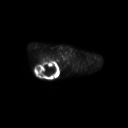
FDG PET of an extremity soft-tissue mass (from a PET/CT study), one axial slice. Slice 209 of 267 in the series (ordered by position). 3.27 mm slice thickness. 128 × 128 image matrix, field of view 700 × 700 mm. Patient: male, 61 years. Case-level facts recorded for this patient, not image findings: histological type: pleiomorphic spindle cell undifferentiated; grade: high; site of the primary tumour: right parascapusular.
Structures marked on this image (expert contour drawn on MRI and transferred to this co-registered scan by the dataset authors):
- gross tumour volume including surrounding oedema: box from (x=34, y=60) to (x=60, y=77) px
- gross tumour volume (mass): (x=35, y=60)–(x=58, y=76)